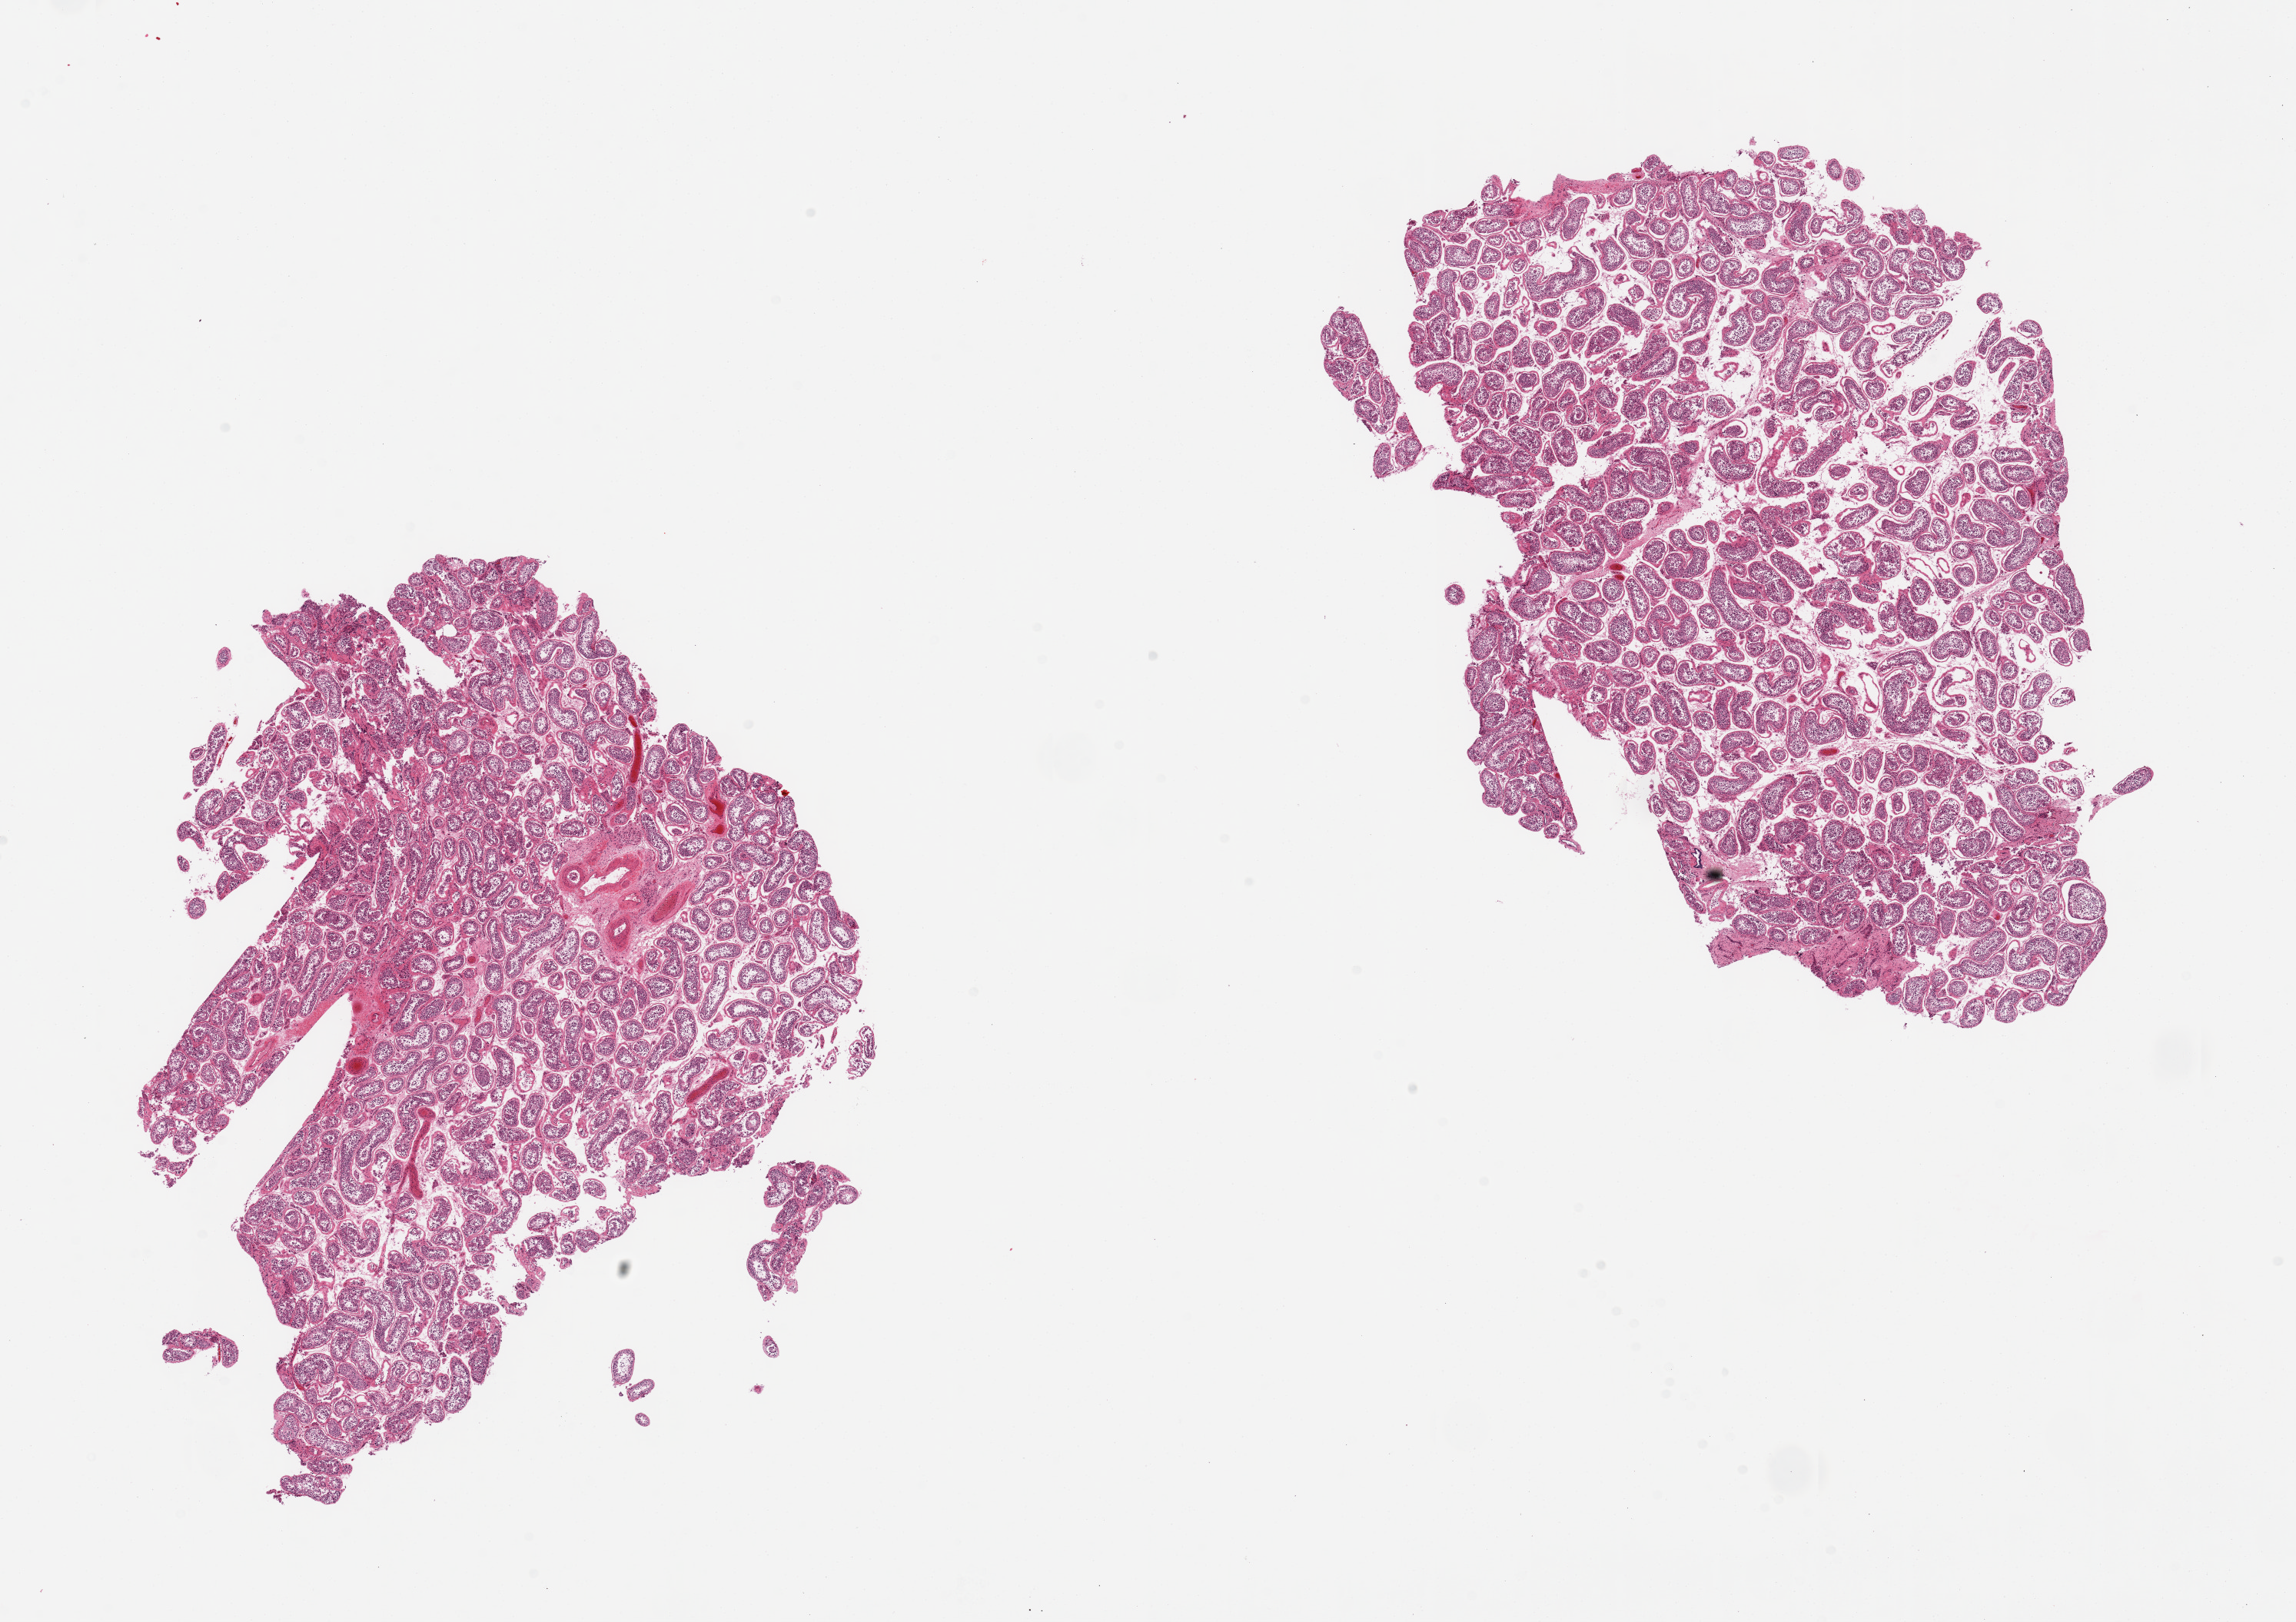
Whole-slide image, H&E stain — a low-resolution overview of the entire scanned area, about 23.6 x 16.7 mm, PAXgene-fixed paraffin-embedded (PFPE) section, target tissue: testis, tissue donor sample.
Reviewer comment on this tissue sample: 2 pieces, mild-moderate autolysis, focally approaching score '2'--spermatogenesis present, appears reduced.